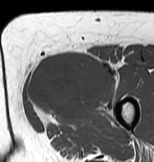
MRI of an extremity soft-tissue mass, one axial slice. Slice 28 of 83 in the series (ordered by position). MR volume resampled by the dataset authors to the PET/CT grid (not the native acquisition matrix). 3.27 mm slice thickness. 154 × 162 image matrix, field of view 150 × 158 mm. Female patient. From the clinical record (not read from this slice): histological type: myxofibrosarcoma; grade: intermediate; site of the primary tumour: left thigh.
Annotated regions visible in this slice (expert contour drawn on MRI and transferred to this co-registered scan by the dataset authors):
- gross tumour volume including surrounding oedema: bounding box <26,52,118,124> (left, top, right, bottom; pixels)
- gross tumour volume (mass): <28,52,116,117>